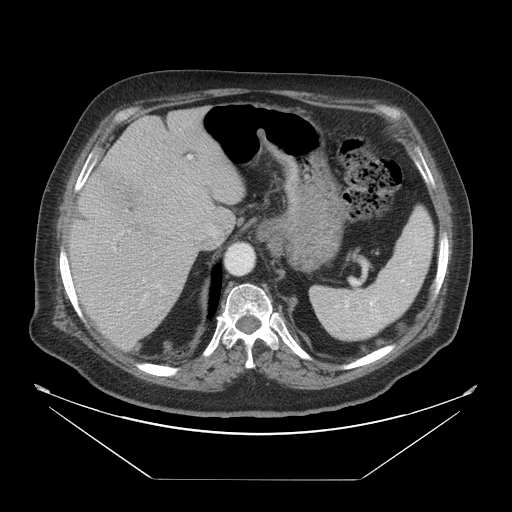
Contrast-enhanced abdominal CT, one axial slice; position 37 of 45 along the scan axis; reconstruction kernel STANDARD; soft-tissue window (W 400 / L 40 HU); 512 × 512 image matrix. Male patient, age 87 years. Case-level facts recorded for this patient, not image findings: diagnosis: colorectal cancer liver metastases, imaged before liver resection.
Outlined on this slice (outlined manually by an expert reader):
- liver: box from (x=70, y=108) to (x=247, y=350) px
- planned liver remnant (the part of the liver to remain after resection): (x=110, y=108)–(x=247, y=207)
- portal vein (with intrahepatic branches): (x=120, y=155)–(x=193, y=287)
- liver metastasis: (x=121, y=222)–(x=146, y=242)
- liver metastasis: (x=95, y=165)–(x=145, y=213)